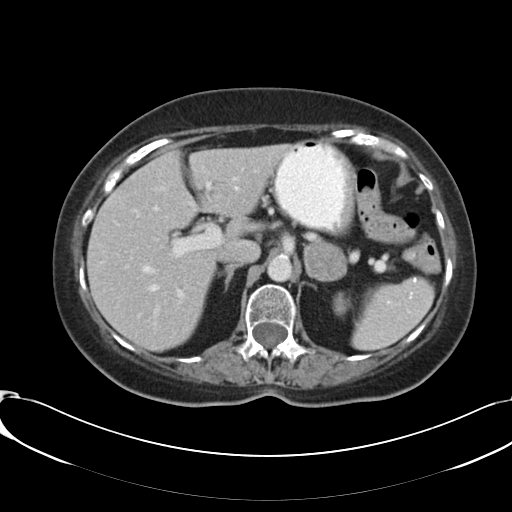
Contrast-enhanced abdominal CT, one axial slice; reconstruction kernel B30f; 120 kVp; intravenous contrast given; soft-tissue window (W 400 / L 40 HU); 5 mm slice thickness; 512 × 512 image matrix, field of view 366 × 366 mm. Patient: female, 73 years. From the clinical record (not read from this slice): diagnosis: adrenocortical carcinoma; tumour side: left adrenal.
Annotated regions visible in this slice (semi-automatically segmented with operator editing):
- mass: box from (x=304, y=241) to (x=347, y=280) px